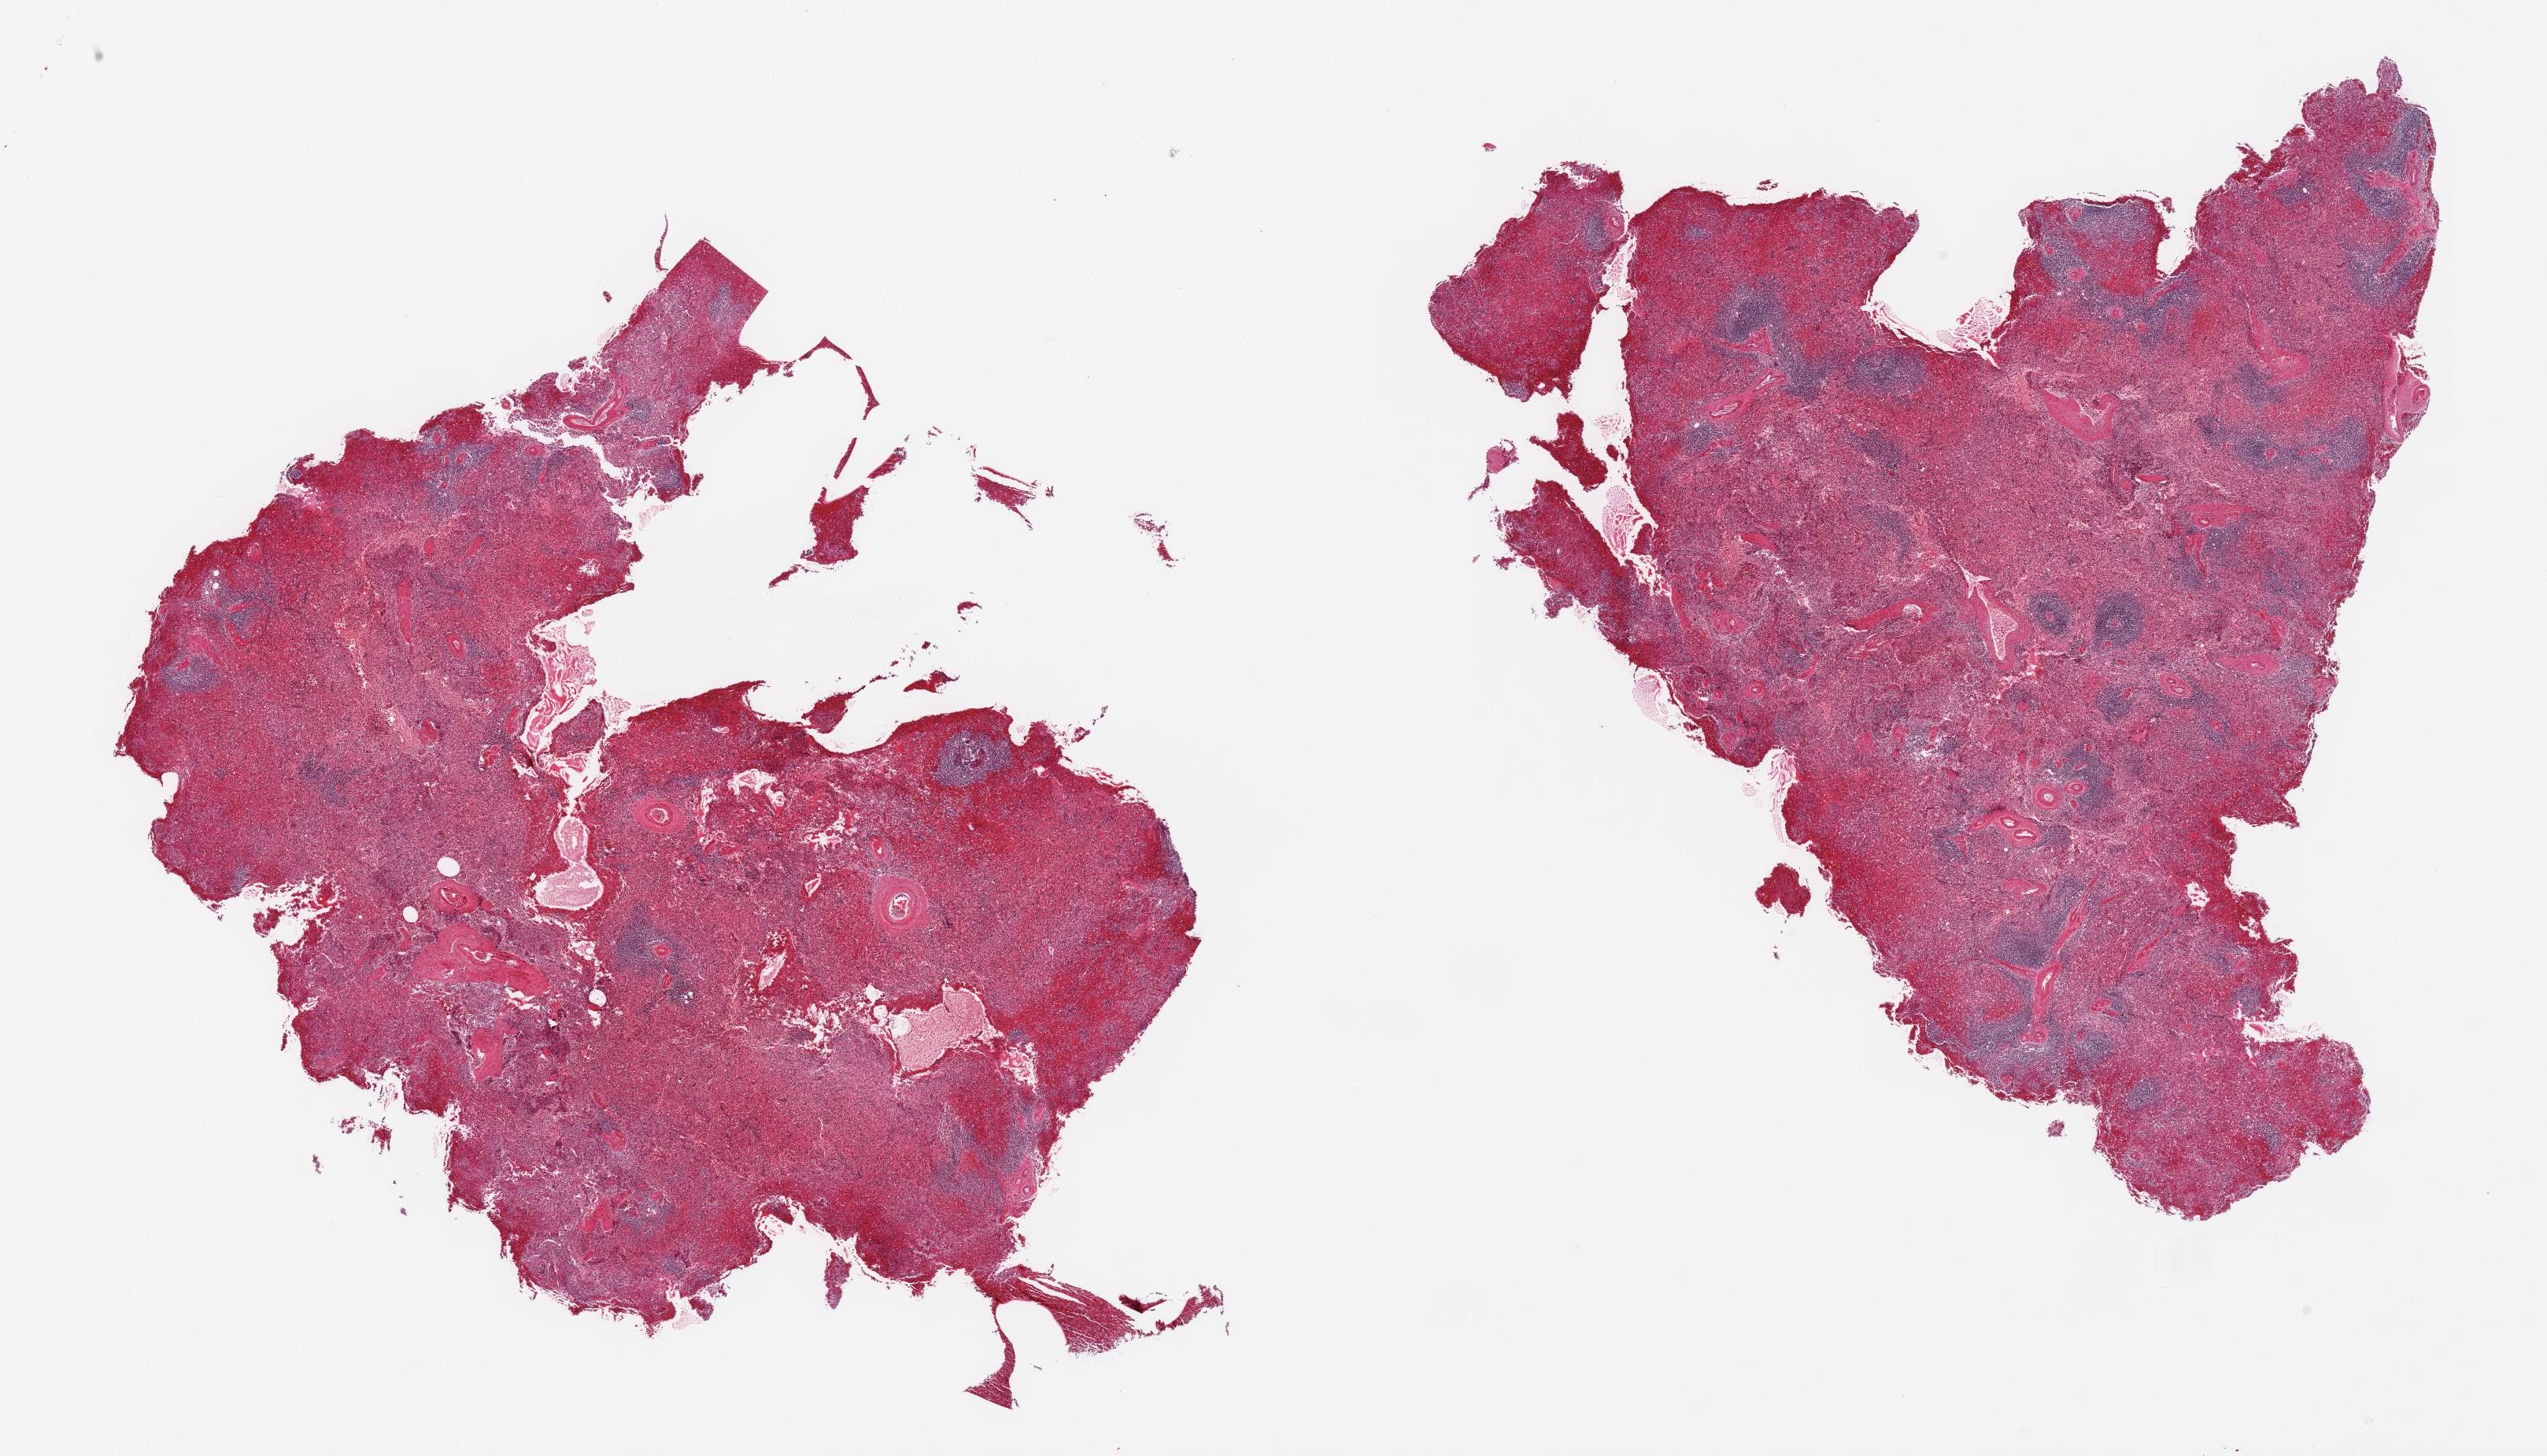
Digitized haematoxylin and eosin-stained section, brightfield — low-resolution overview of the scanned area, about 25.6 x 14.6 mm; PAXgene-fixed, paraffin-embedded tissue; section of spleen (target tissue); tissue donor sample. Donor sex: female.
* reviewer comment on this tissue sample: 2 pieces; partly fragmented